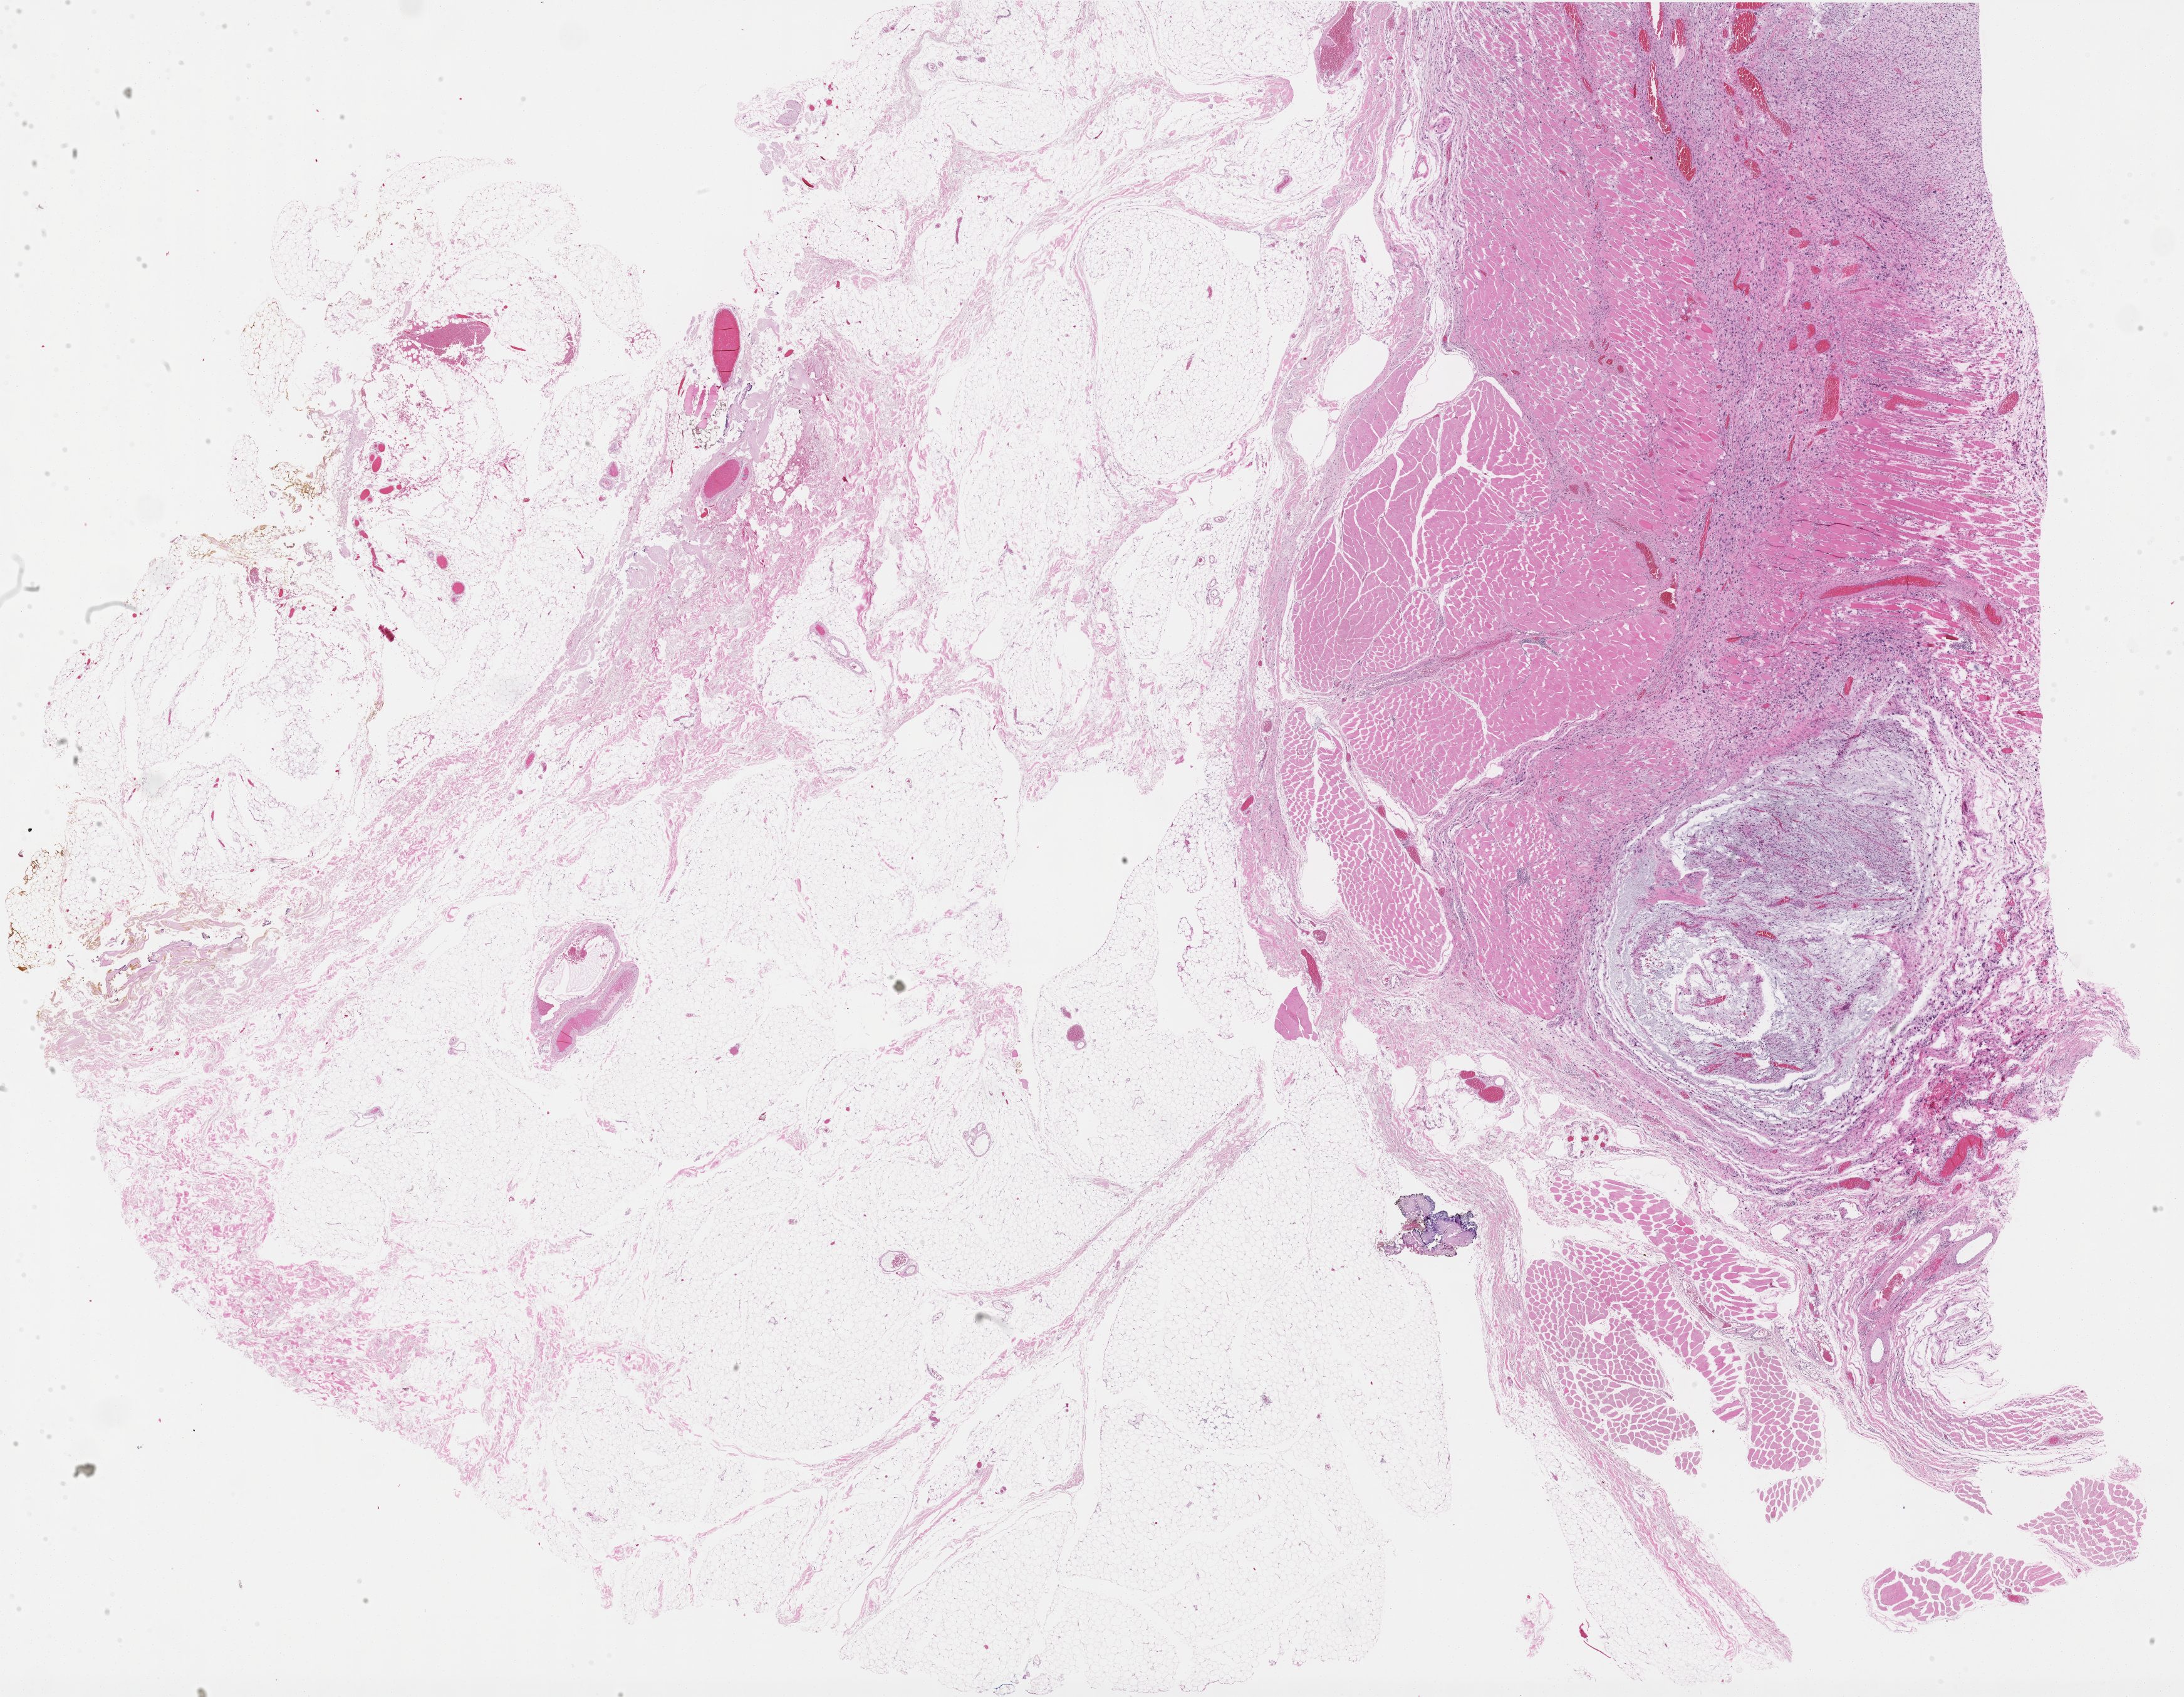
Digitized H&E tissue section (whole slide) — a low-resolution overview of the entire scanned area, about 28.0 x 21.8 mm (slide scanned at 40x), FFPE section, connective, subcutaneous and other soft tissues, primary tumour sample. Male patient; age at initial diagnosis 75 years.
- histologic diagnosis: Fibromyxosarcoma (connective, subcutaneous and other soft tissues of thorax)